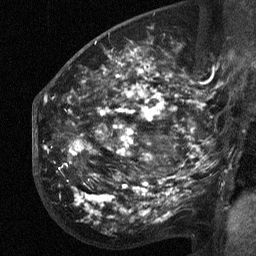
Breast MRI (dynamic contrast-enhanced), one sagittal slice; dynamic contrast-enhanced study with each time point stored as its own series, time point 2 of 3 at this slice position (early post-contrast, ordered by acquisition time); 1.5 T; TE 4.8 ms, TR 27 ms; 2.3 mm slice thickness; 256 × 256 image matrix, field of view 200 × 200 mm. Patient: female, 50 years. Case-level facts recorded for this patient, not image findings: setting: breast cancer imaged before/during neoadjuvant chemotherapy; receptor status: HER2-positive.
Annotated regions visible in this slice (semi-automatic segmentation, software-assisted and operator-edited):
- analysis volume of interest (the breast-tissue region the enhancement analysis was run in; not a lesion): bounding box (x1, y1, x2, y2) in pixels: (53, 64, 211, 218)
- tumour enhancement mask (voxels above the 90 % enhancement threshold inside the analysis volume of interest): (70, 70, 203, 186)